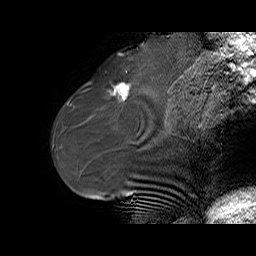
Breast MRI (dynamic contrast-enhanced), one sagittal slice; dynamic contrast-enhanced series, time point 2 of 6 at this slice position (early post-contrast); 1.5 T; TE 5.5 ms, TR 32.9 ms; 4 mm slice thickness; 256 × 256 image matrix. Female patient. From the clinical record (not read from this slice): setting: breast cancer imaged before/during neoadjuvant chemotherapy; receptor status: HER2-positive.
Structures marked on this image (semi-automatically segmented with operator editing):
- analysis volume of interest (the breast-tissue region the enhancement analysis was run in; not a lesion): bounding box [x1, y1, x2, y2] px = [96, 73, 141, 111]
- tumour enhancement mask (voxels above the 100 % enhancement threshold inside the analysis volume of interest): [114, 83, 130, 100]